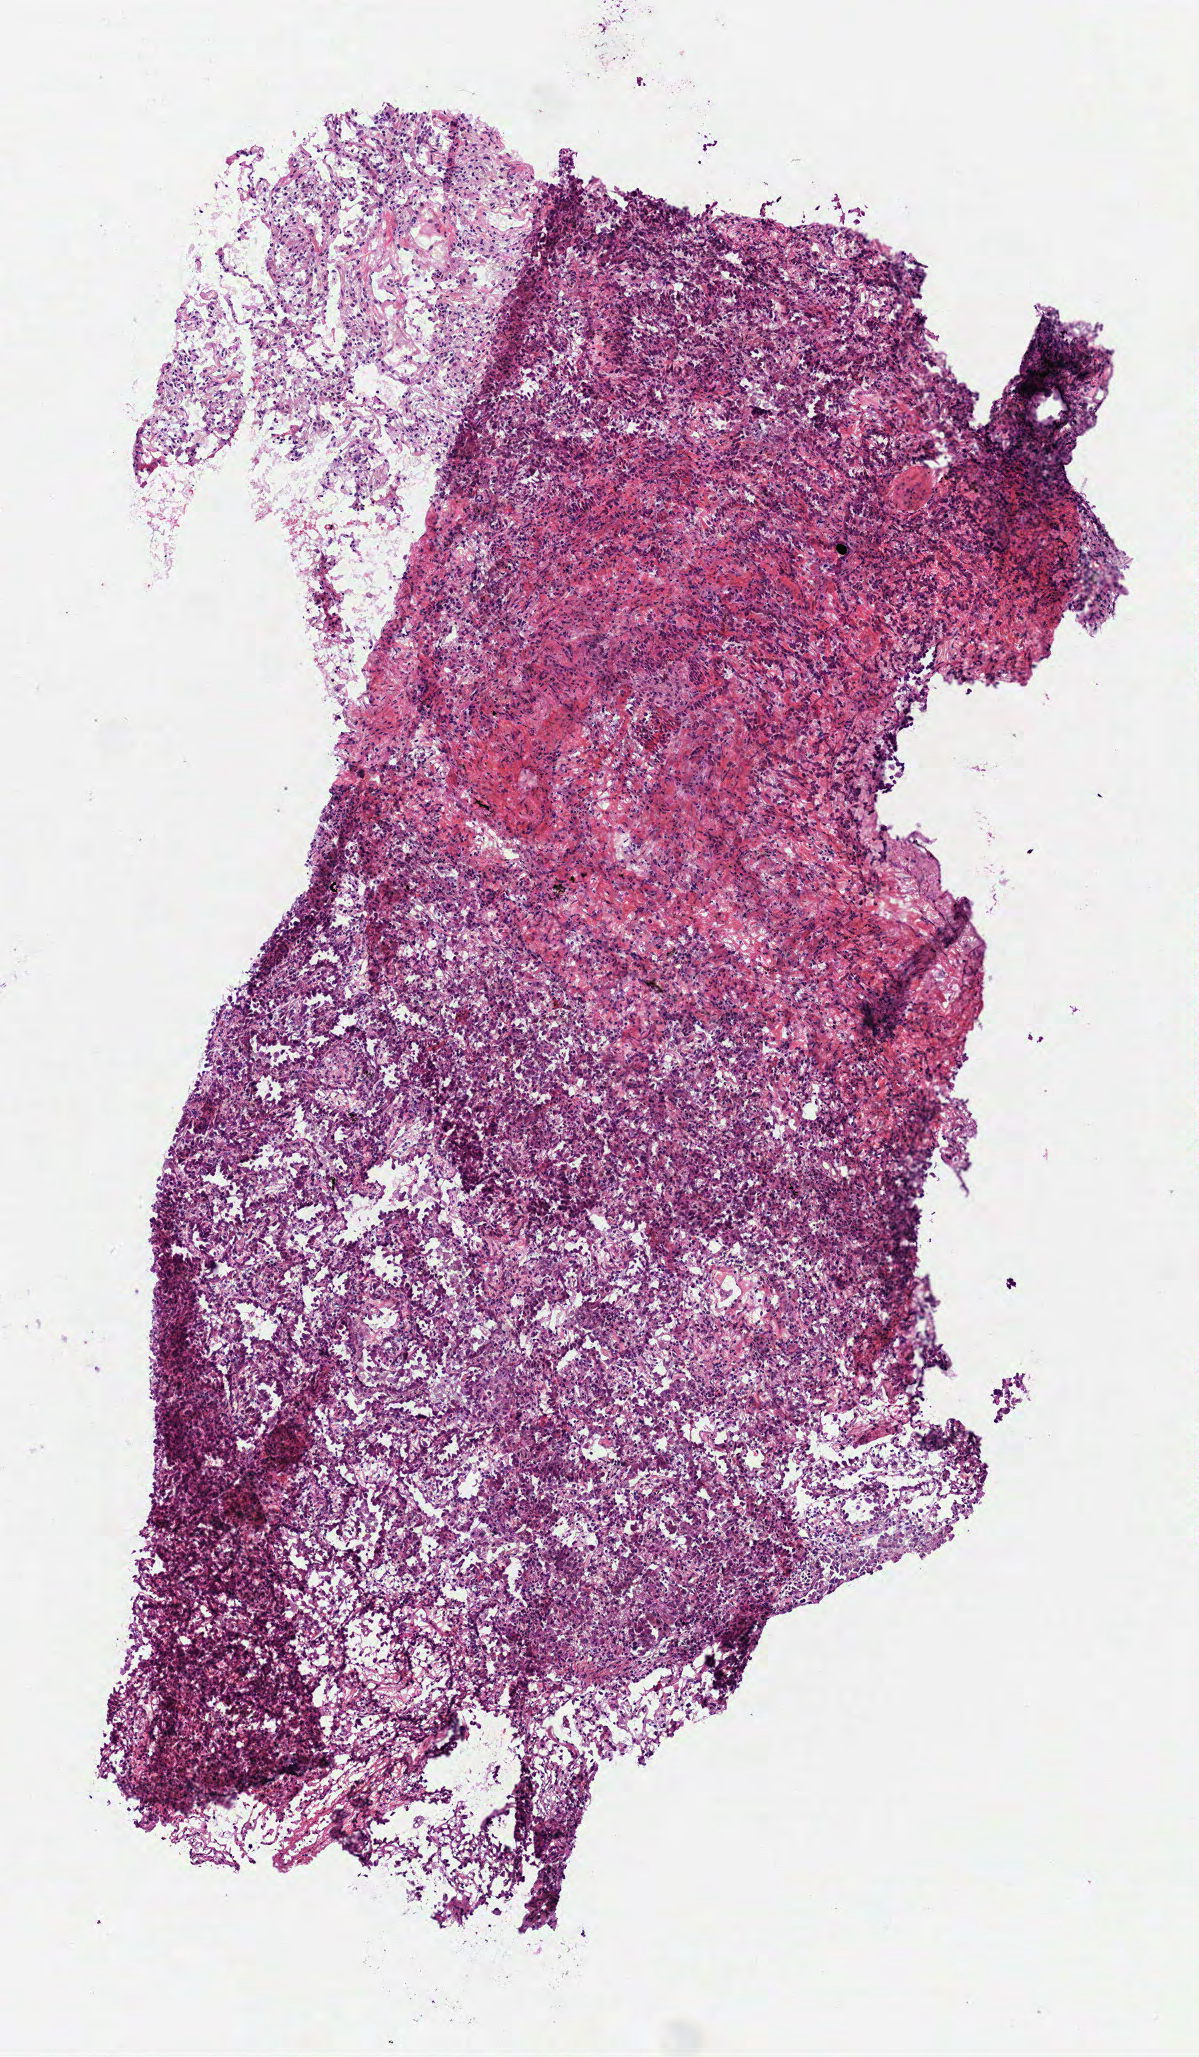
Digitized Hematoxylin and eosin (H&E) stained tissue section (whole slide) — whole scanned area (about 2.4 x 4.1 mm, from a 40x scan) shown as a low-resolution overview, frozen section from the top of the tissue portion, lung, primary tumour sample. Patient: female, age at initial diagnosis 63 years. Slide review estimates, as recorded: tumour cells 75%, tumour nuclei 75%, normal cells 15%, stromal cells 10%, necrosis 0%.
- histologic diagnosis: Bronchiolo-alveolar carcinoma, non-mucinous (lower lobe, lung)
- AJCC pathologic stage: IB (7th edition)
- laterality: left